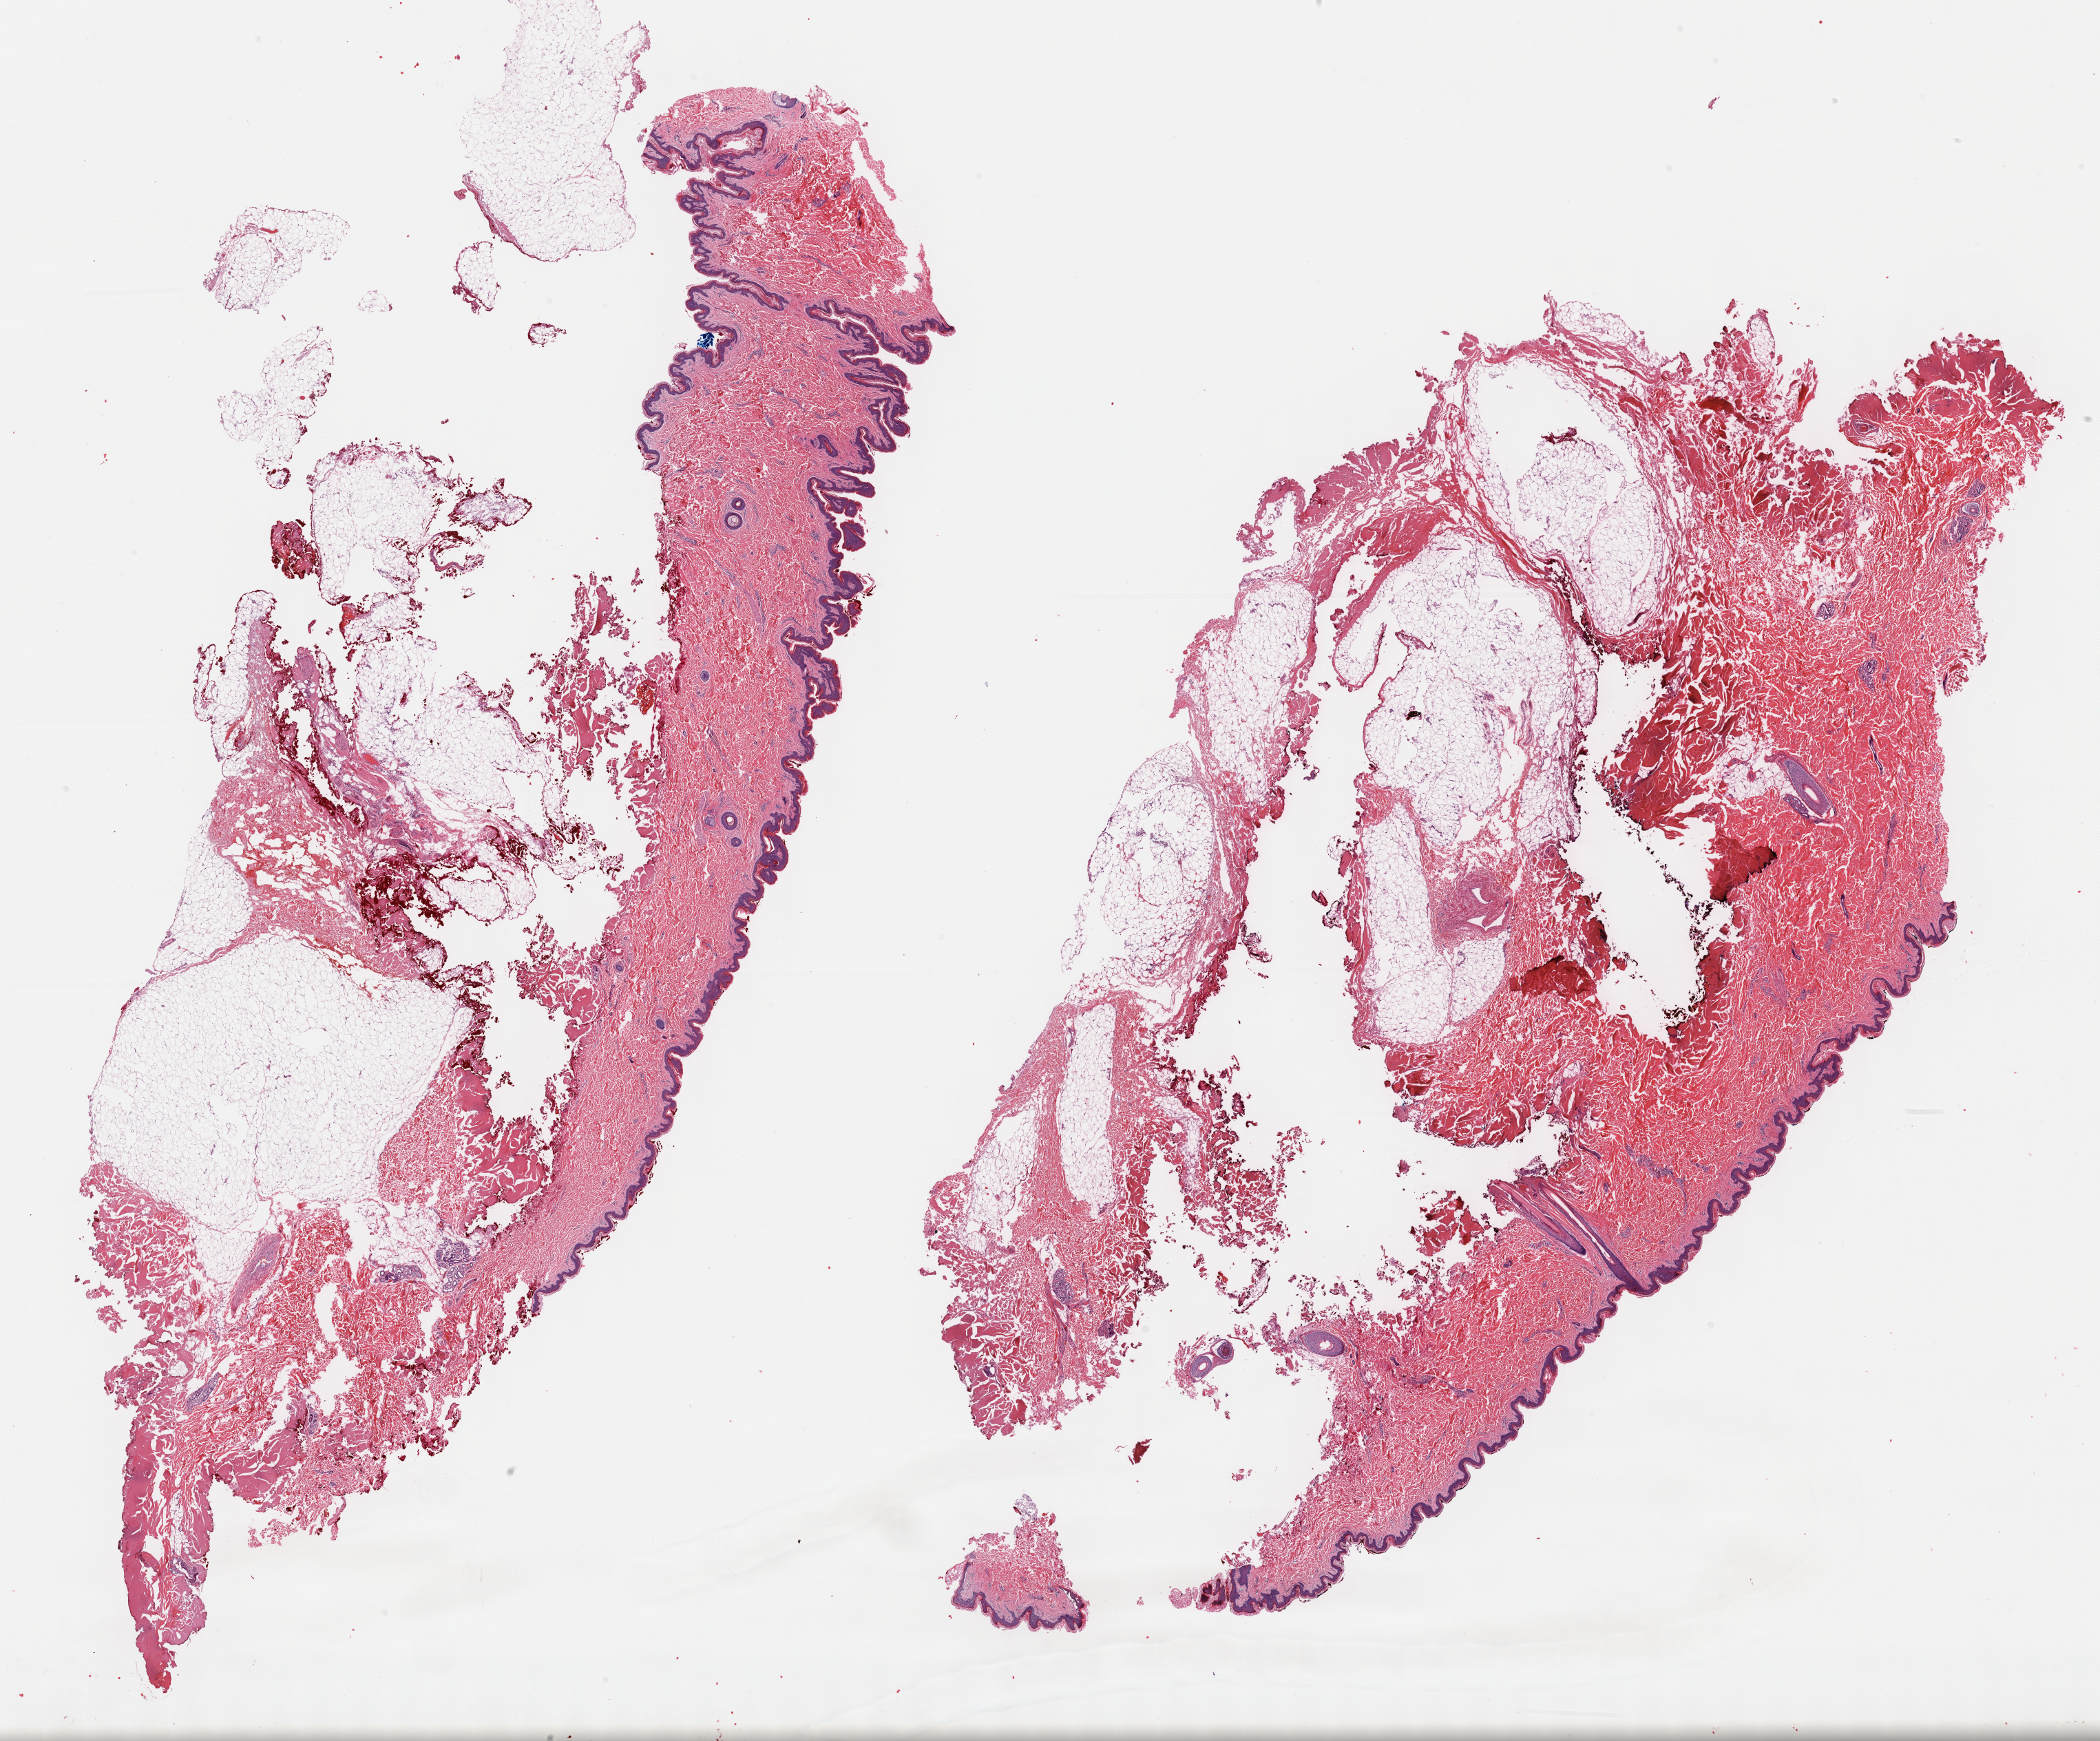
H&E whole-slide image, shown as a low-resolution overview of the whole scanned area (about 24.7 x 20.5 mm, slide scanned at 40x); formalin-fixed paraffin-embedded (FFPE) diagnostic section; primary tumour sample from the connective, subcutaneous and other soft tissues. Patient: male, age at initial diagnosis 35 years.
Histologic diagnosis: Fibromyxosarcoma (connective, subcutaneous and other soft tissues of lower limb and hip).